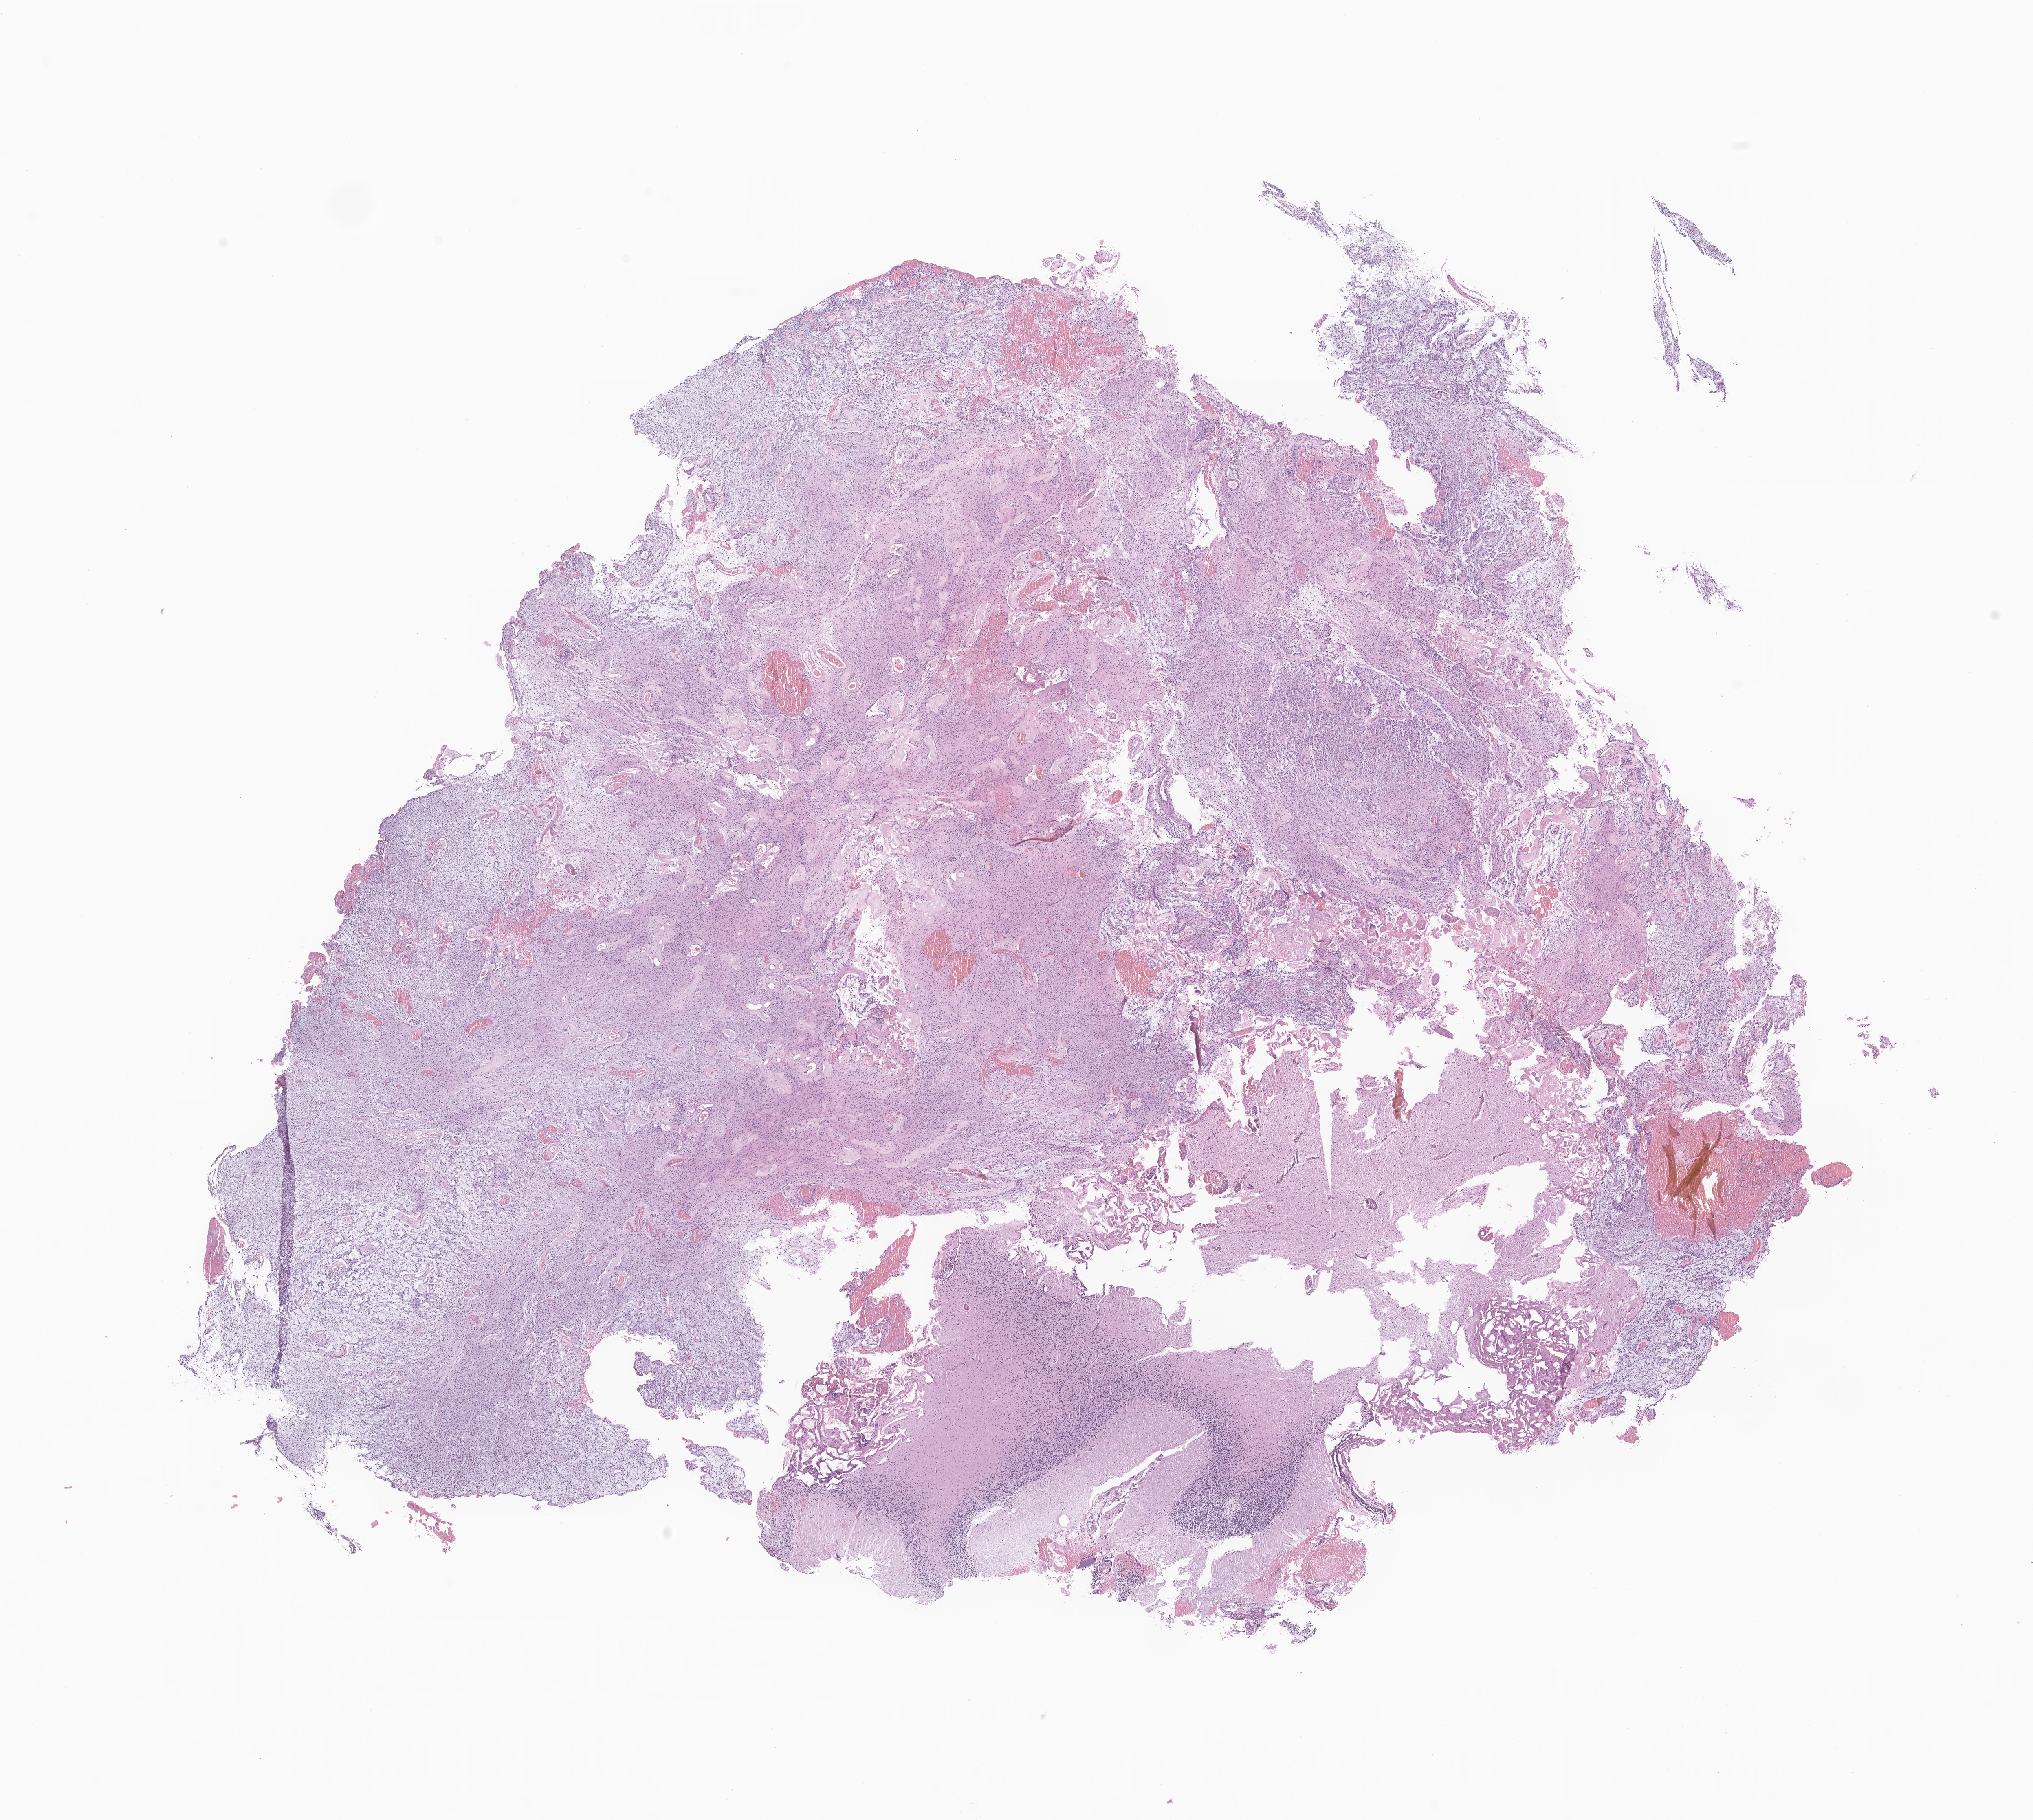
Digitized haematoxylin and eosin-stained section of tumor tissue from the cerebellum — whole scanned area (about 21.0 x 18.8 mm) shown as a low-resolution overview; formalin-fixed paraffin-embedded section. Patient: male, age 105 months (8 years 9 months).
Diagnosis (ICD-O-3 morphology term): Pilocytic astrocytoma.